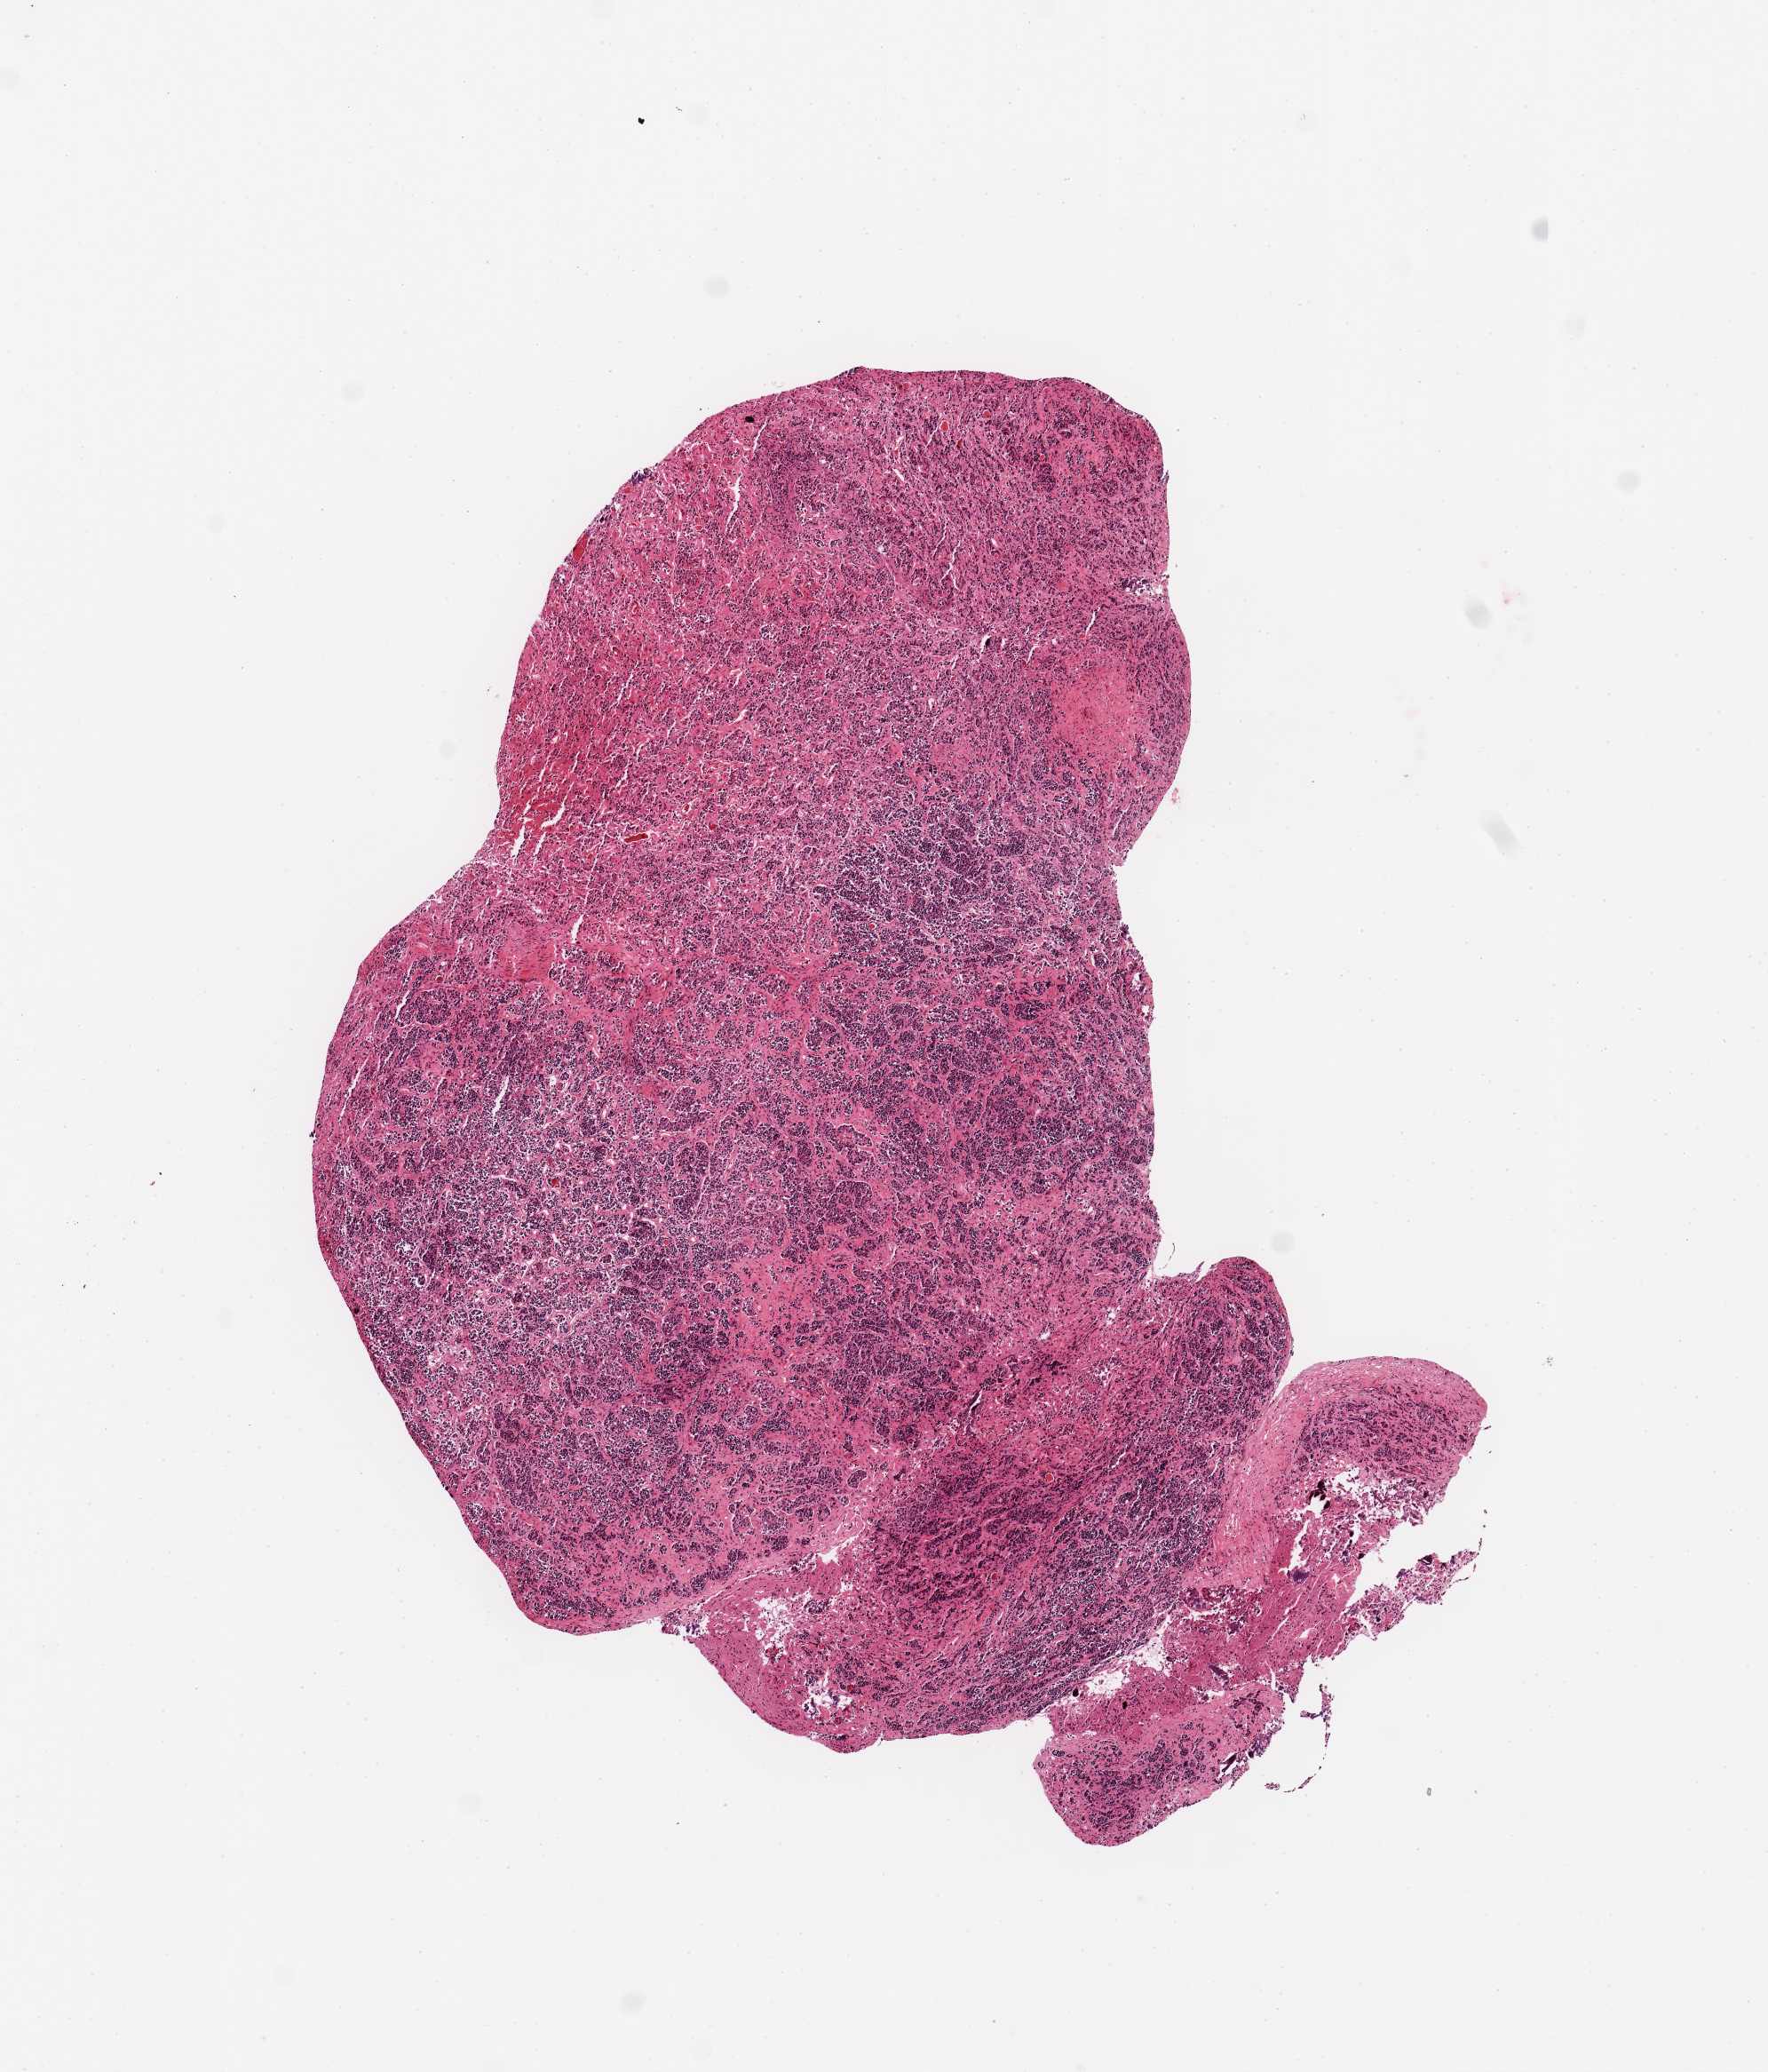
Digitized haematoxylin and eosin-stained section — whole scanned area (about 7.9 x 9.2 mm) shown as a low-resolution overview; PAXgene-fixed, paraffin-embedded tissue; section of pituitary (target tissue); tissue donor sample. Male donor.
- pathologist's review note for this sample: 1 piece, all adenohypophysis